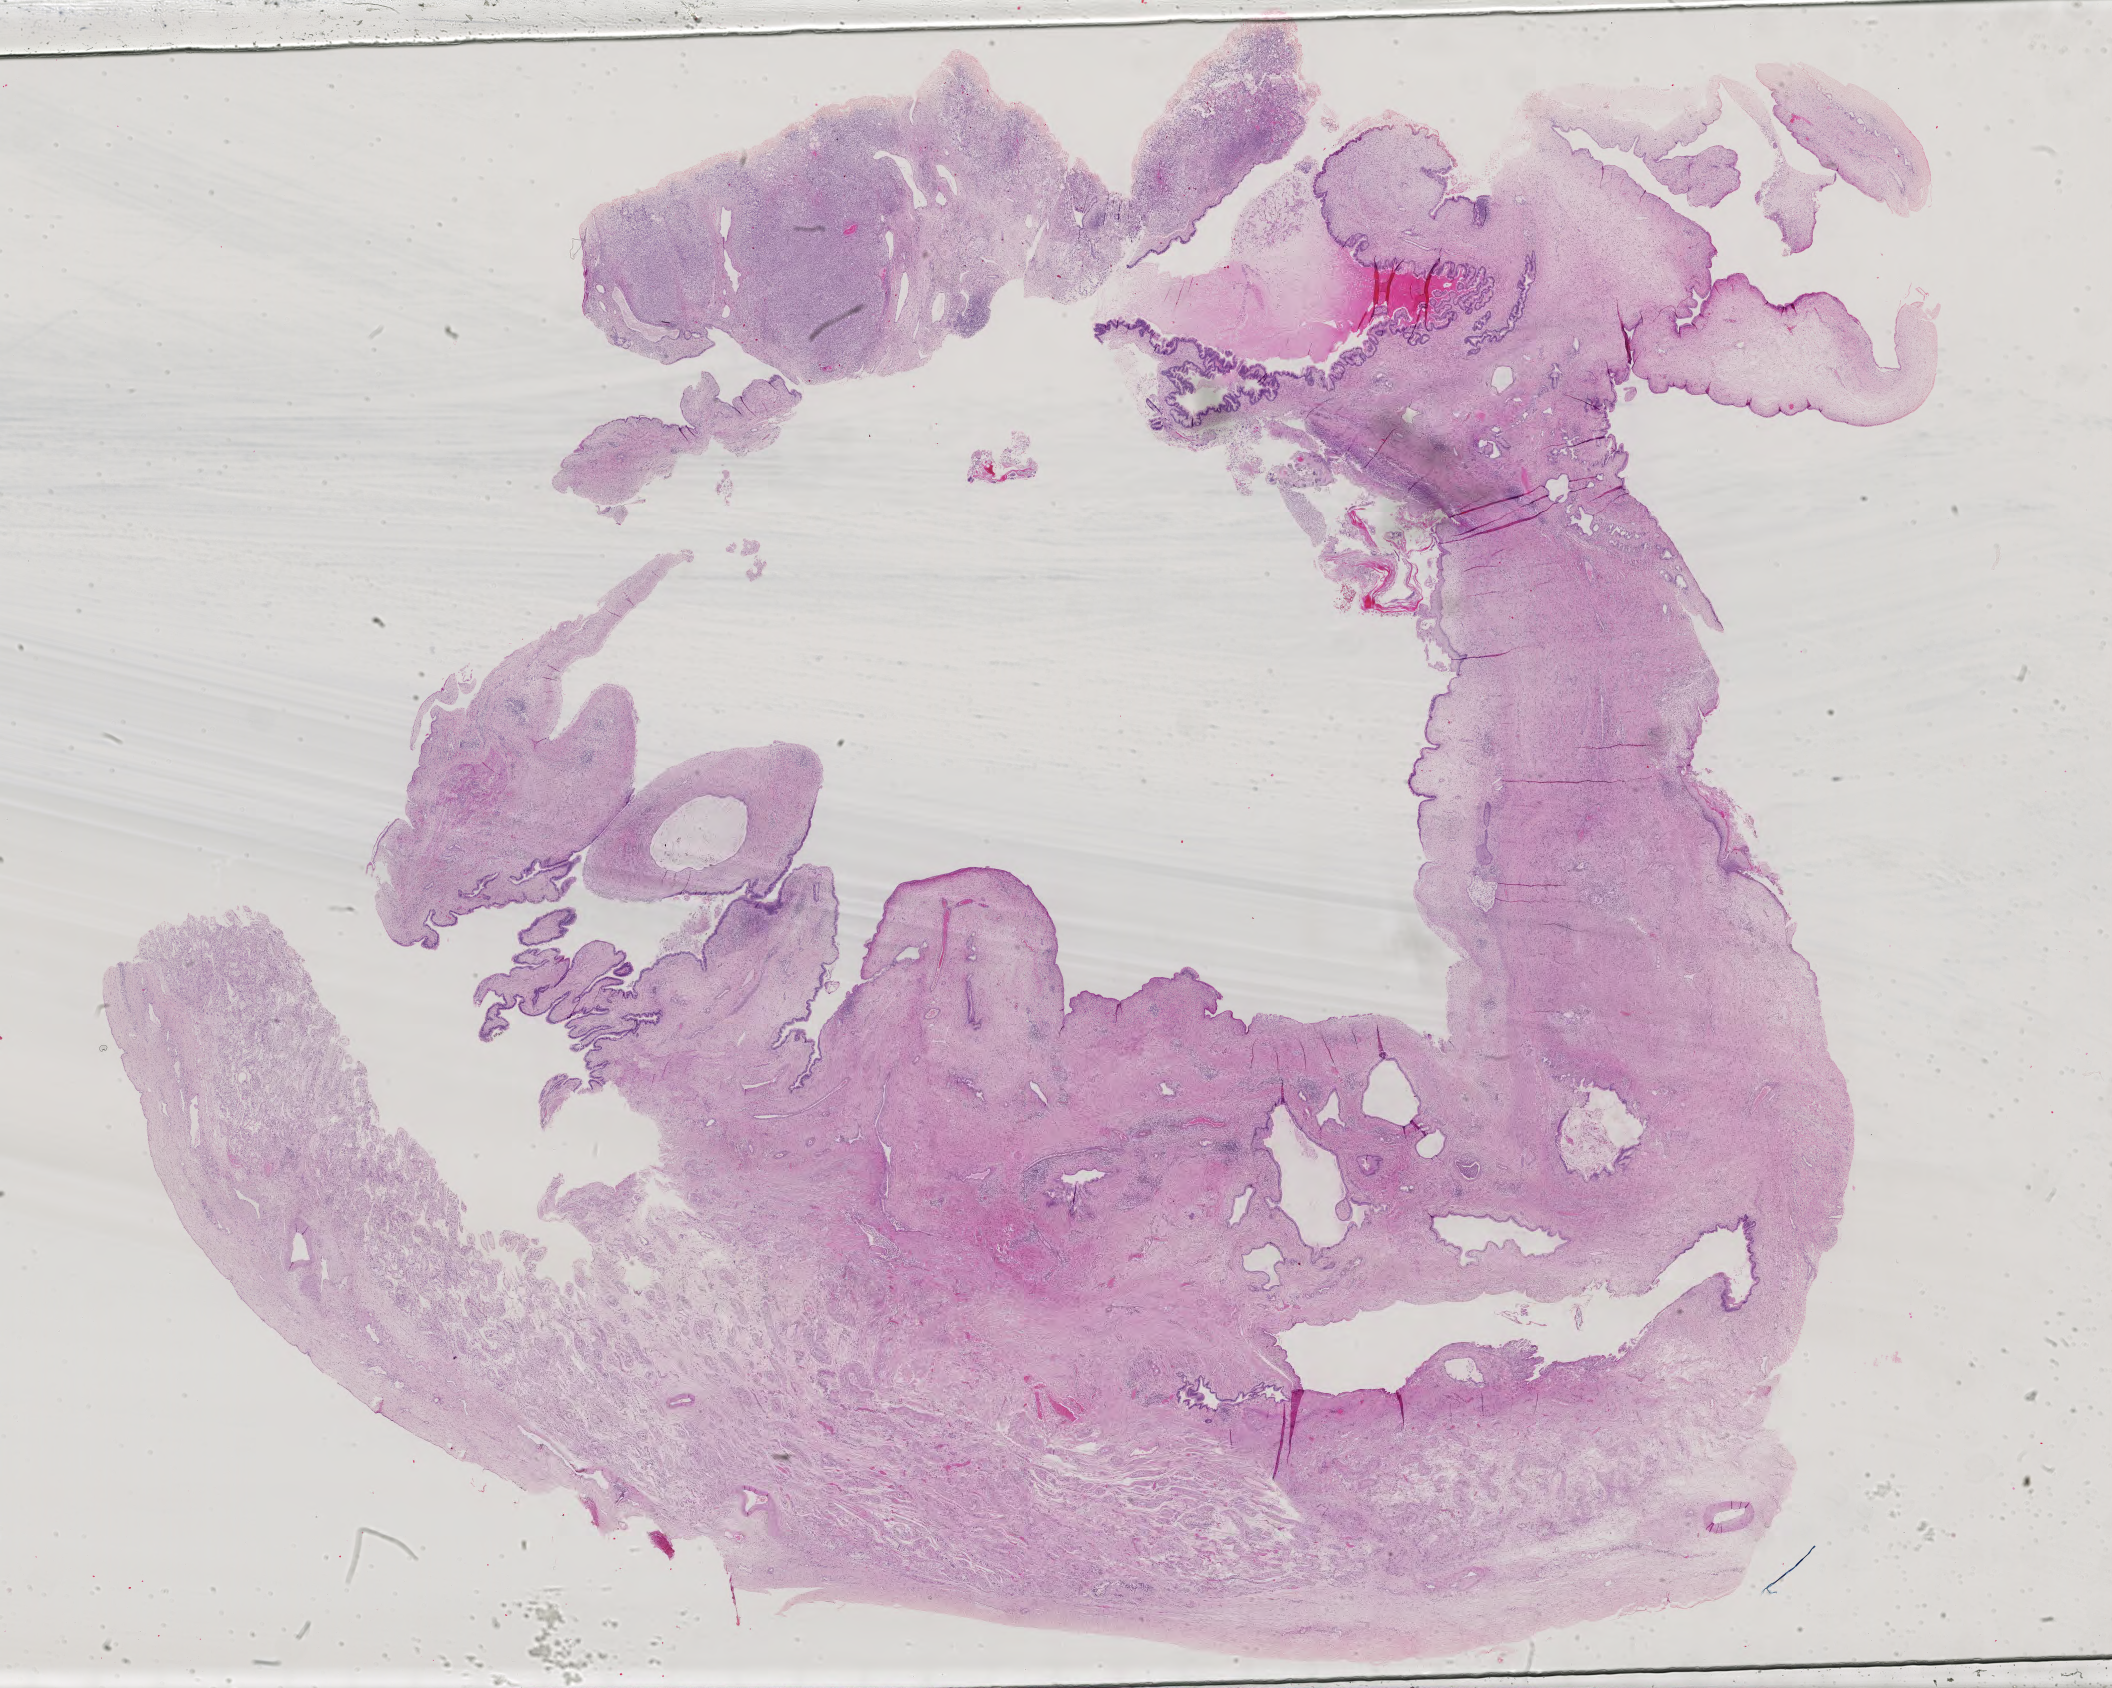
Digitized H&E tissue section (whole slide), low-resolution overview of the scanned area, about 30.8 x 24.6 mm (from a 40x scan), FFPE section, testis, primary tumour sample. Patient: male, age at initial diagnosis 30 years.
Pathologic diagnosis: Mixed germ cell tumor. TNM: T2 NX M0. AJCC pathologic stage: IS (5th edition).